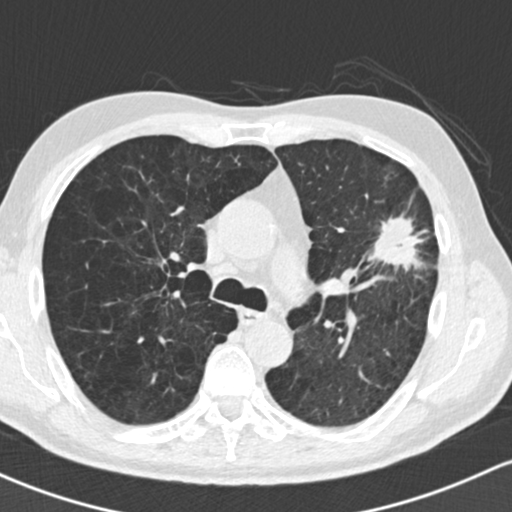
Low-dose screening chest CT, one axial slice. Position 100 of 162 along the scan axis. 120 kVp. Lung window (W 1500 / L -600 HU). 2 mm slice thickness. 512 × 512 image matrix, field of view 318 × 318 mm.
Structures marked on this image (outlined manually by an expert reader):
- lesion 1 (tumor, upper lobe of left lung): bounding box [x1, y1, x2, y2] px = [362, 214, 427, 271]